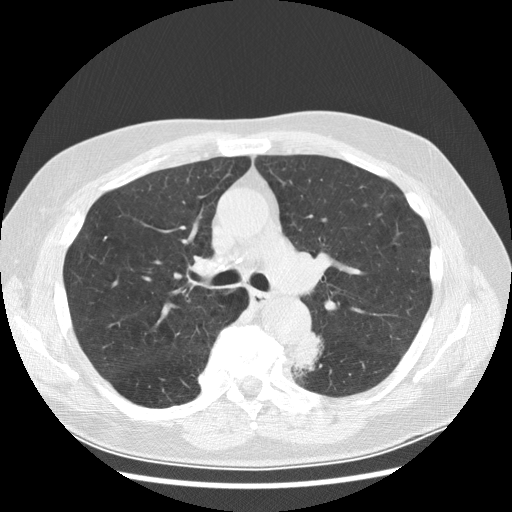
Low-dose screening chest CT, axial slice, first (baseline) screen, lung window (W 1500 / L -600 HU), 512 × 512 image matrix. Male, age 70 years at enrolment.
- Expert reader's lesion annotation, bounding box <277,333,327,380> (left, top, right, bottom; pixels).
- Reader record for this screening exam (exam-level; its link to the box is not recorded): non-calcified nodule or mass ≥4 mm, left lower lobe, 27 × 16 mm, spiculated (stellate) margins, soft tissue attenuation, pre-existing on the prior screen: yes; interval growth: yes.
- Official screen result: positive, change unspecified: nodule(s) >= 4 mm or enlarging nodule(s), mass(es), or other non-specific abnormalities suspicious for lung cancer.